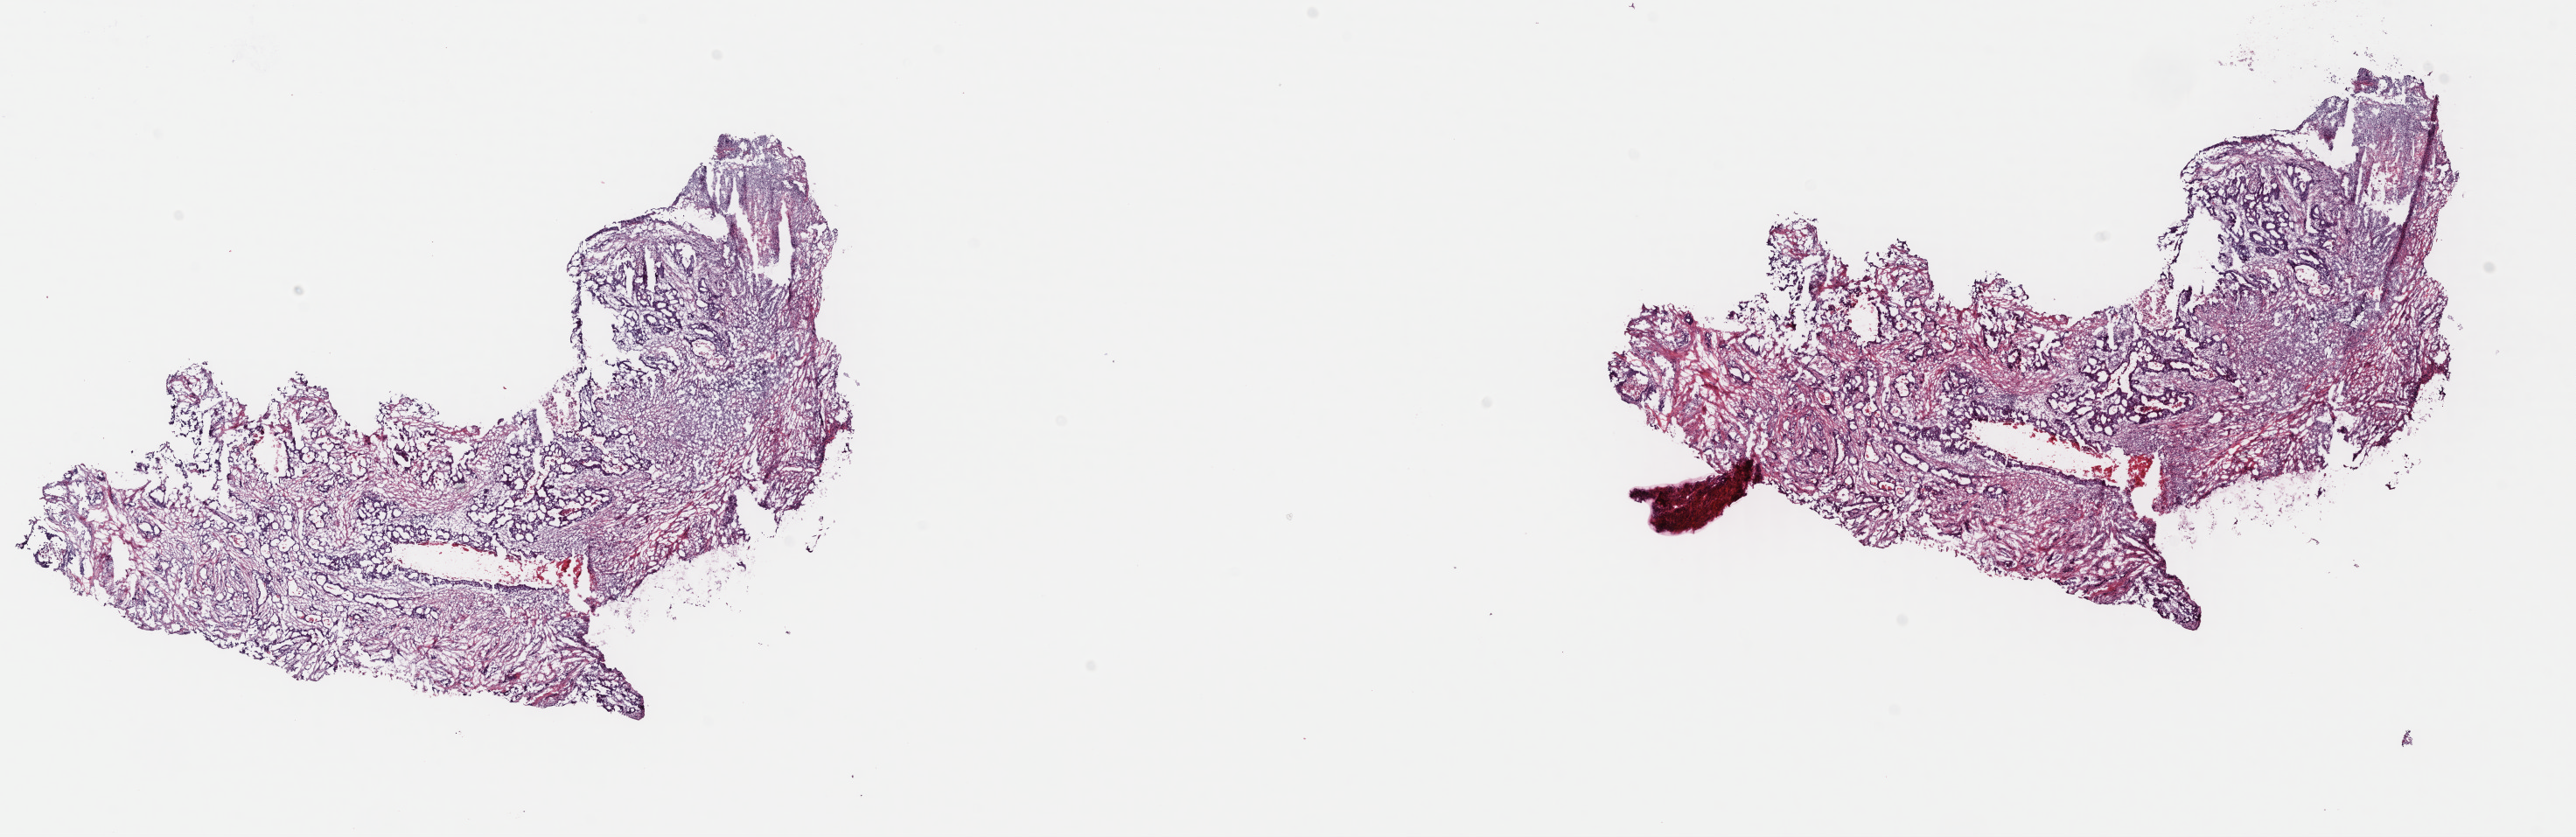
H&E-stained whole-slide image — a low-resolution overview of the entire scanned area, about 23.1 x 7.5 mm (from a 40x scan). Frozen section. Primary tumour sample from the stomach. Patient: male, age at initial diagnosis 73 years. Histologic grade: G3 (poorly differentiated). Slide review estimates, as recorded: tumour cells 93%, tumour nuclei 65%, normal cells 0%, stromal cells 0%, necrosis 7%. Inflammatory infiltration, as recorded: lymphocyte infiltration 5%, monocyte infiltration 0%, neutrophil infiltration 0%.
• AJCC pathologic stage: IIIA (7th edition)
• diagnosis: Adenocarcinoma, intestinal type (cardia, NOS)
• lymph nodes positive (case pathology): 4 of 16 examined